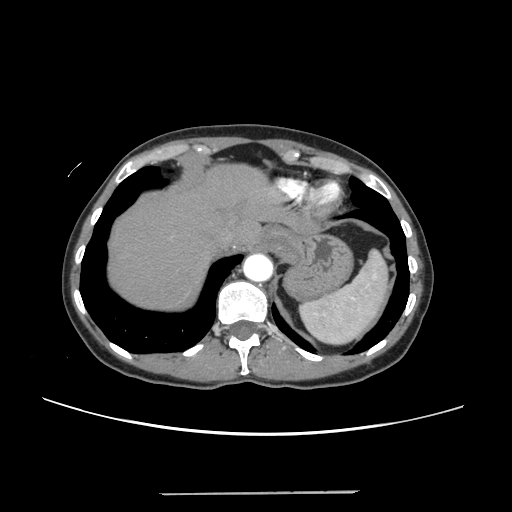
Contrast-enhanced abdominal CT, one axial slice; slice 208 of 240 in the series (ordered by position); 120 kVp; intravenous contrast given; soft-tissue window (W 400 / L 40 HU); 1.25 mm slice thickness; 512 × 512 image matrix. Female patient, age 60 years. Case-level facts recorded for this patient, not image findings: diagnosis: colorectal cancer liver metastases, imaged before liver resection; multiple liver metastases: no; largest metastasis: 1.5 cm.
Annotated regions visible in this slice (outlined manually by an expert reader):
- hepatic veins: bounding box (x1, y1, x2, y2) in pixels: (221, 225, 250, 242)
- liver: (108, 166, 287, 309)
- planned liver remnant (the part of the liver to remain after resection): (108, 165, 287, 309)